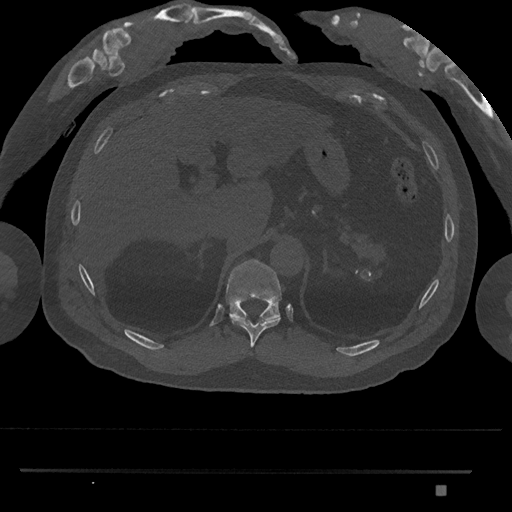
CT including the spine, one axial slice. Position 974 of 1134 along the scan axis. Reconstruction kernel Br40s/3. Bone window (W 1800 / L 400 HU). 0.5 mm slice thickness. 512 × 512 image matrix, field of view 429 × 429 mm. Patient: male, 65 years. Case-level facts recorded for this patient, not image findings: primary cancer: prostate.
Outlined on this slice (semi-automatic segmentation, software-assisted and operator-edited):
- T10 vertebra: bounding box [x1, y1, x2, y2] px = [231, 317, 281, 348]
- T11 vertebra: [225, 259, 282, 319]